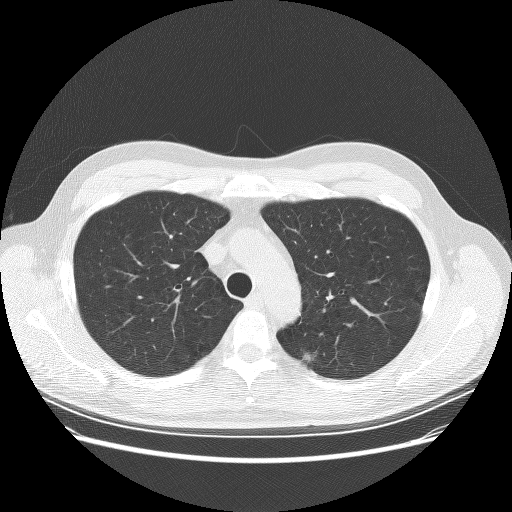
Low-dose screening chest CT, one axial slice; slice 199 of 253 in the series (ordered by position); 120 kVp; lung window (W 1500 / L -600 HU); 2.5 mm slice thickness; 512 × 512 image matrix, field of view 370 × 370 mm.
Annotated regions visible in this slice (manually delineated by an expert):
- lesion 2 (nodule): bounding box <304,353,313,361> (left, top, right, bottom; pixels)